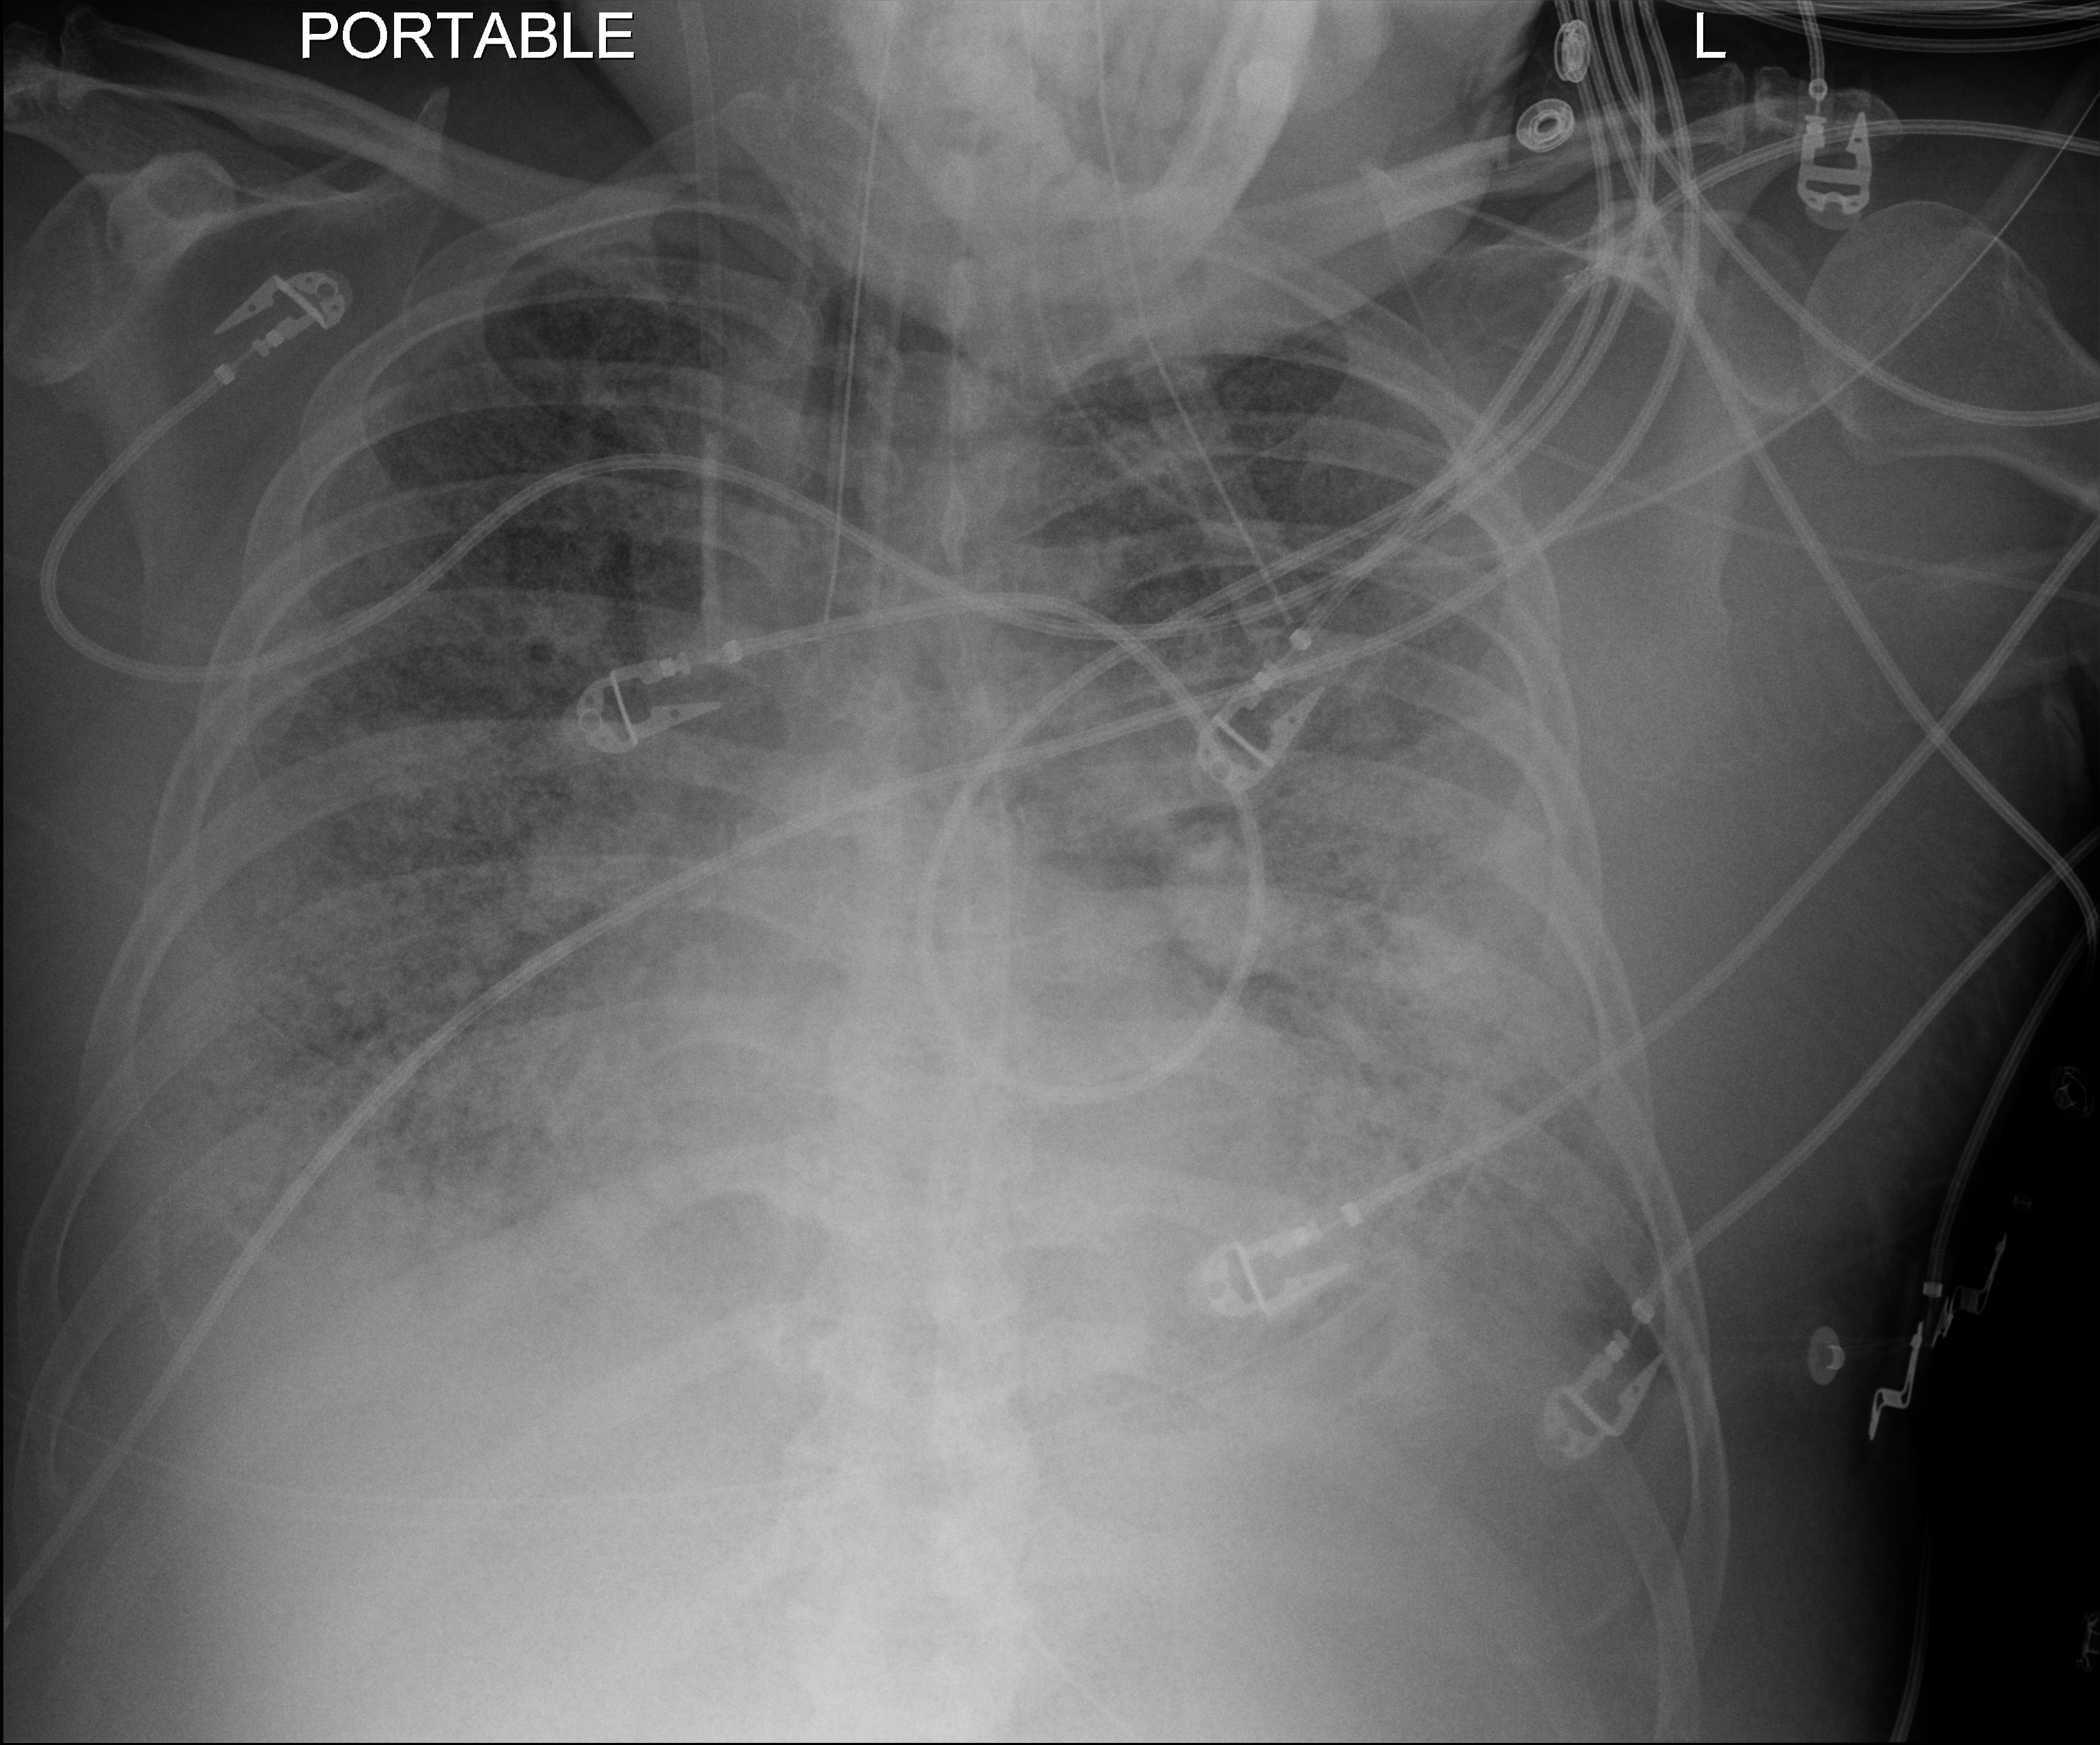
Chest X-ray (portable); anteroposterior (AP) projection. Patient hospitalised with COVID-19; male, aged 60–74 years.
From the hospital-stay record, not from the radiograph (when in the stay this image was taken is not recorded): COPD (admission record): no; mechanically ventilated during this hospital stay: yes.